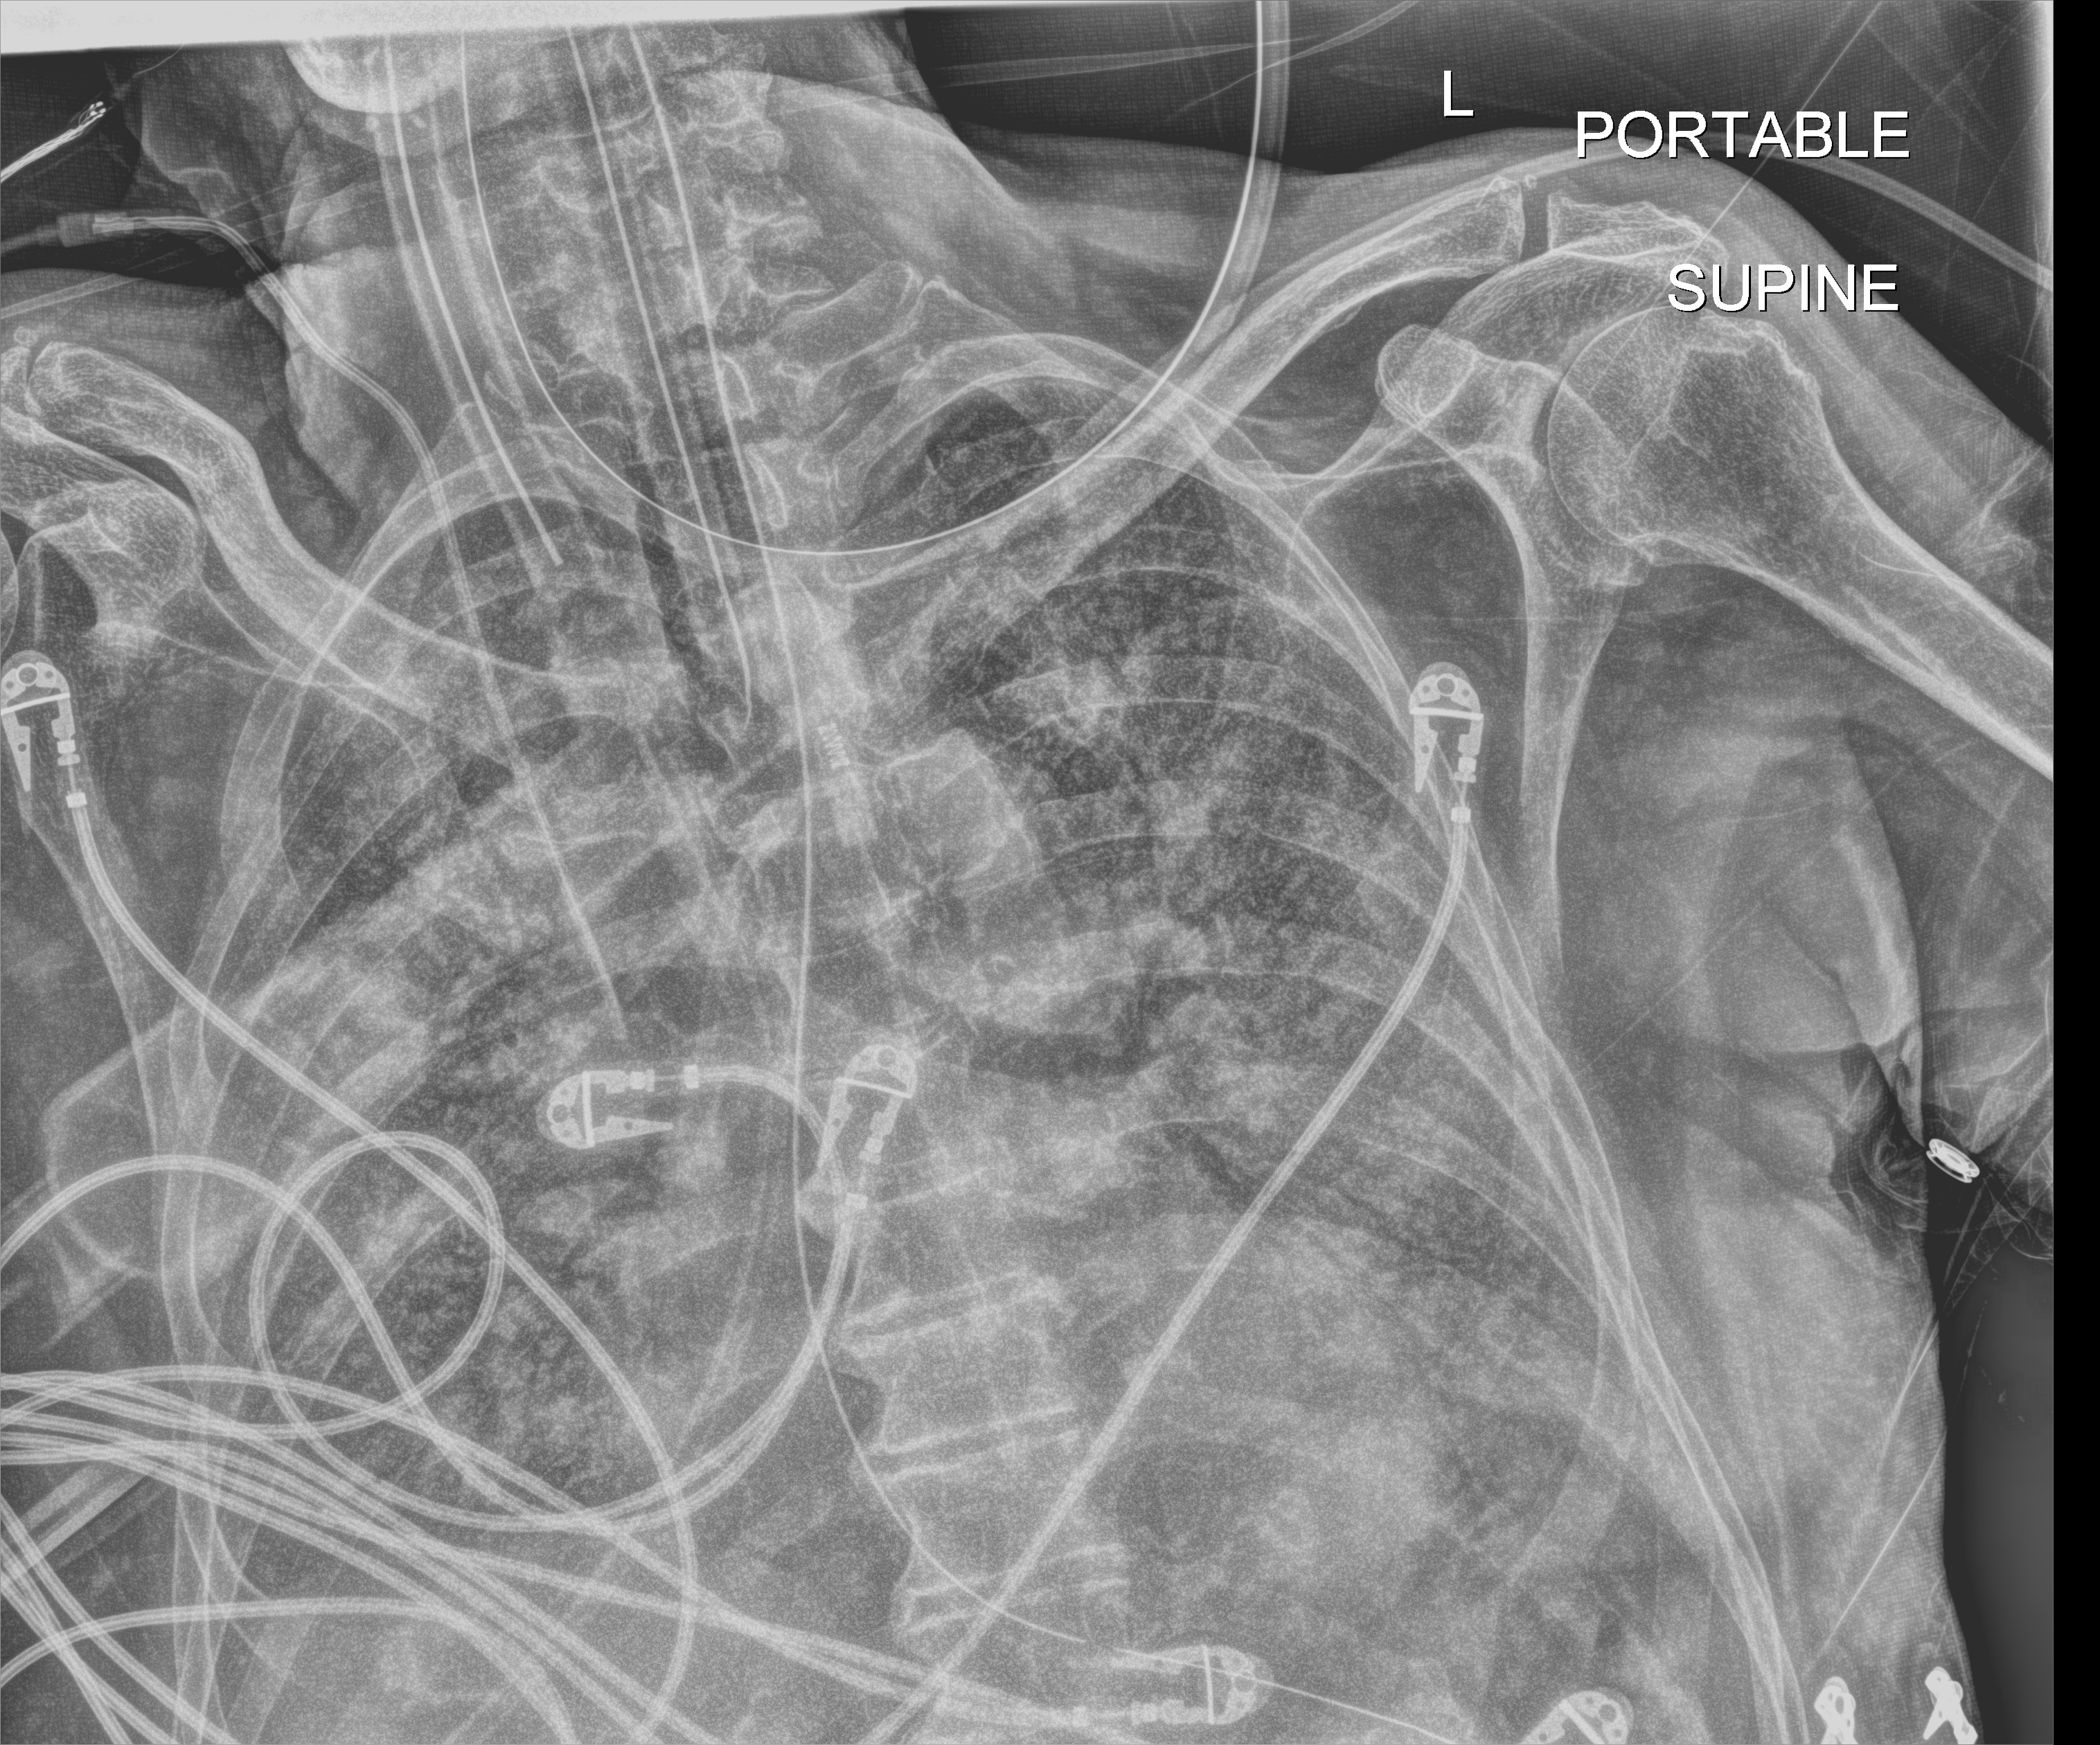
Portable chest radiograph, anteroposterior (AP) projection. Male patient hospitalised with COVID-19, age 75–90 years.
From the hospital-stay record, not from the radiograph (when in the stay this image was taken is not recorded):
- smoking status (admission record): never
- mechanically ventilated during this hospital stay: yes